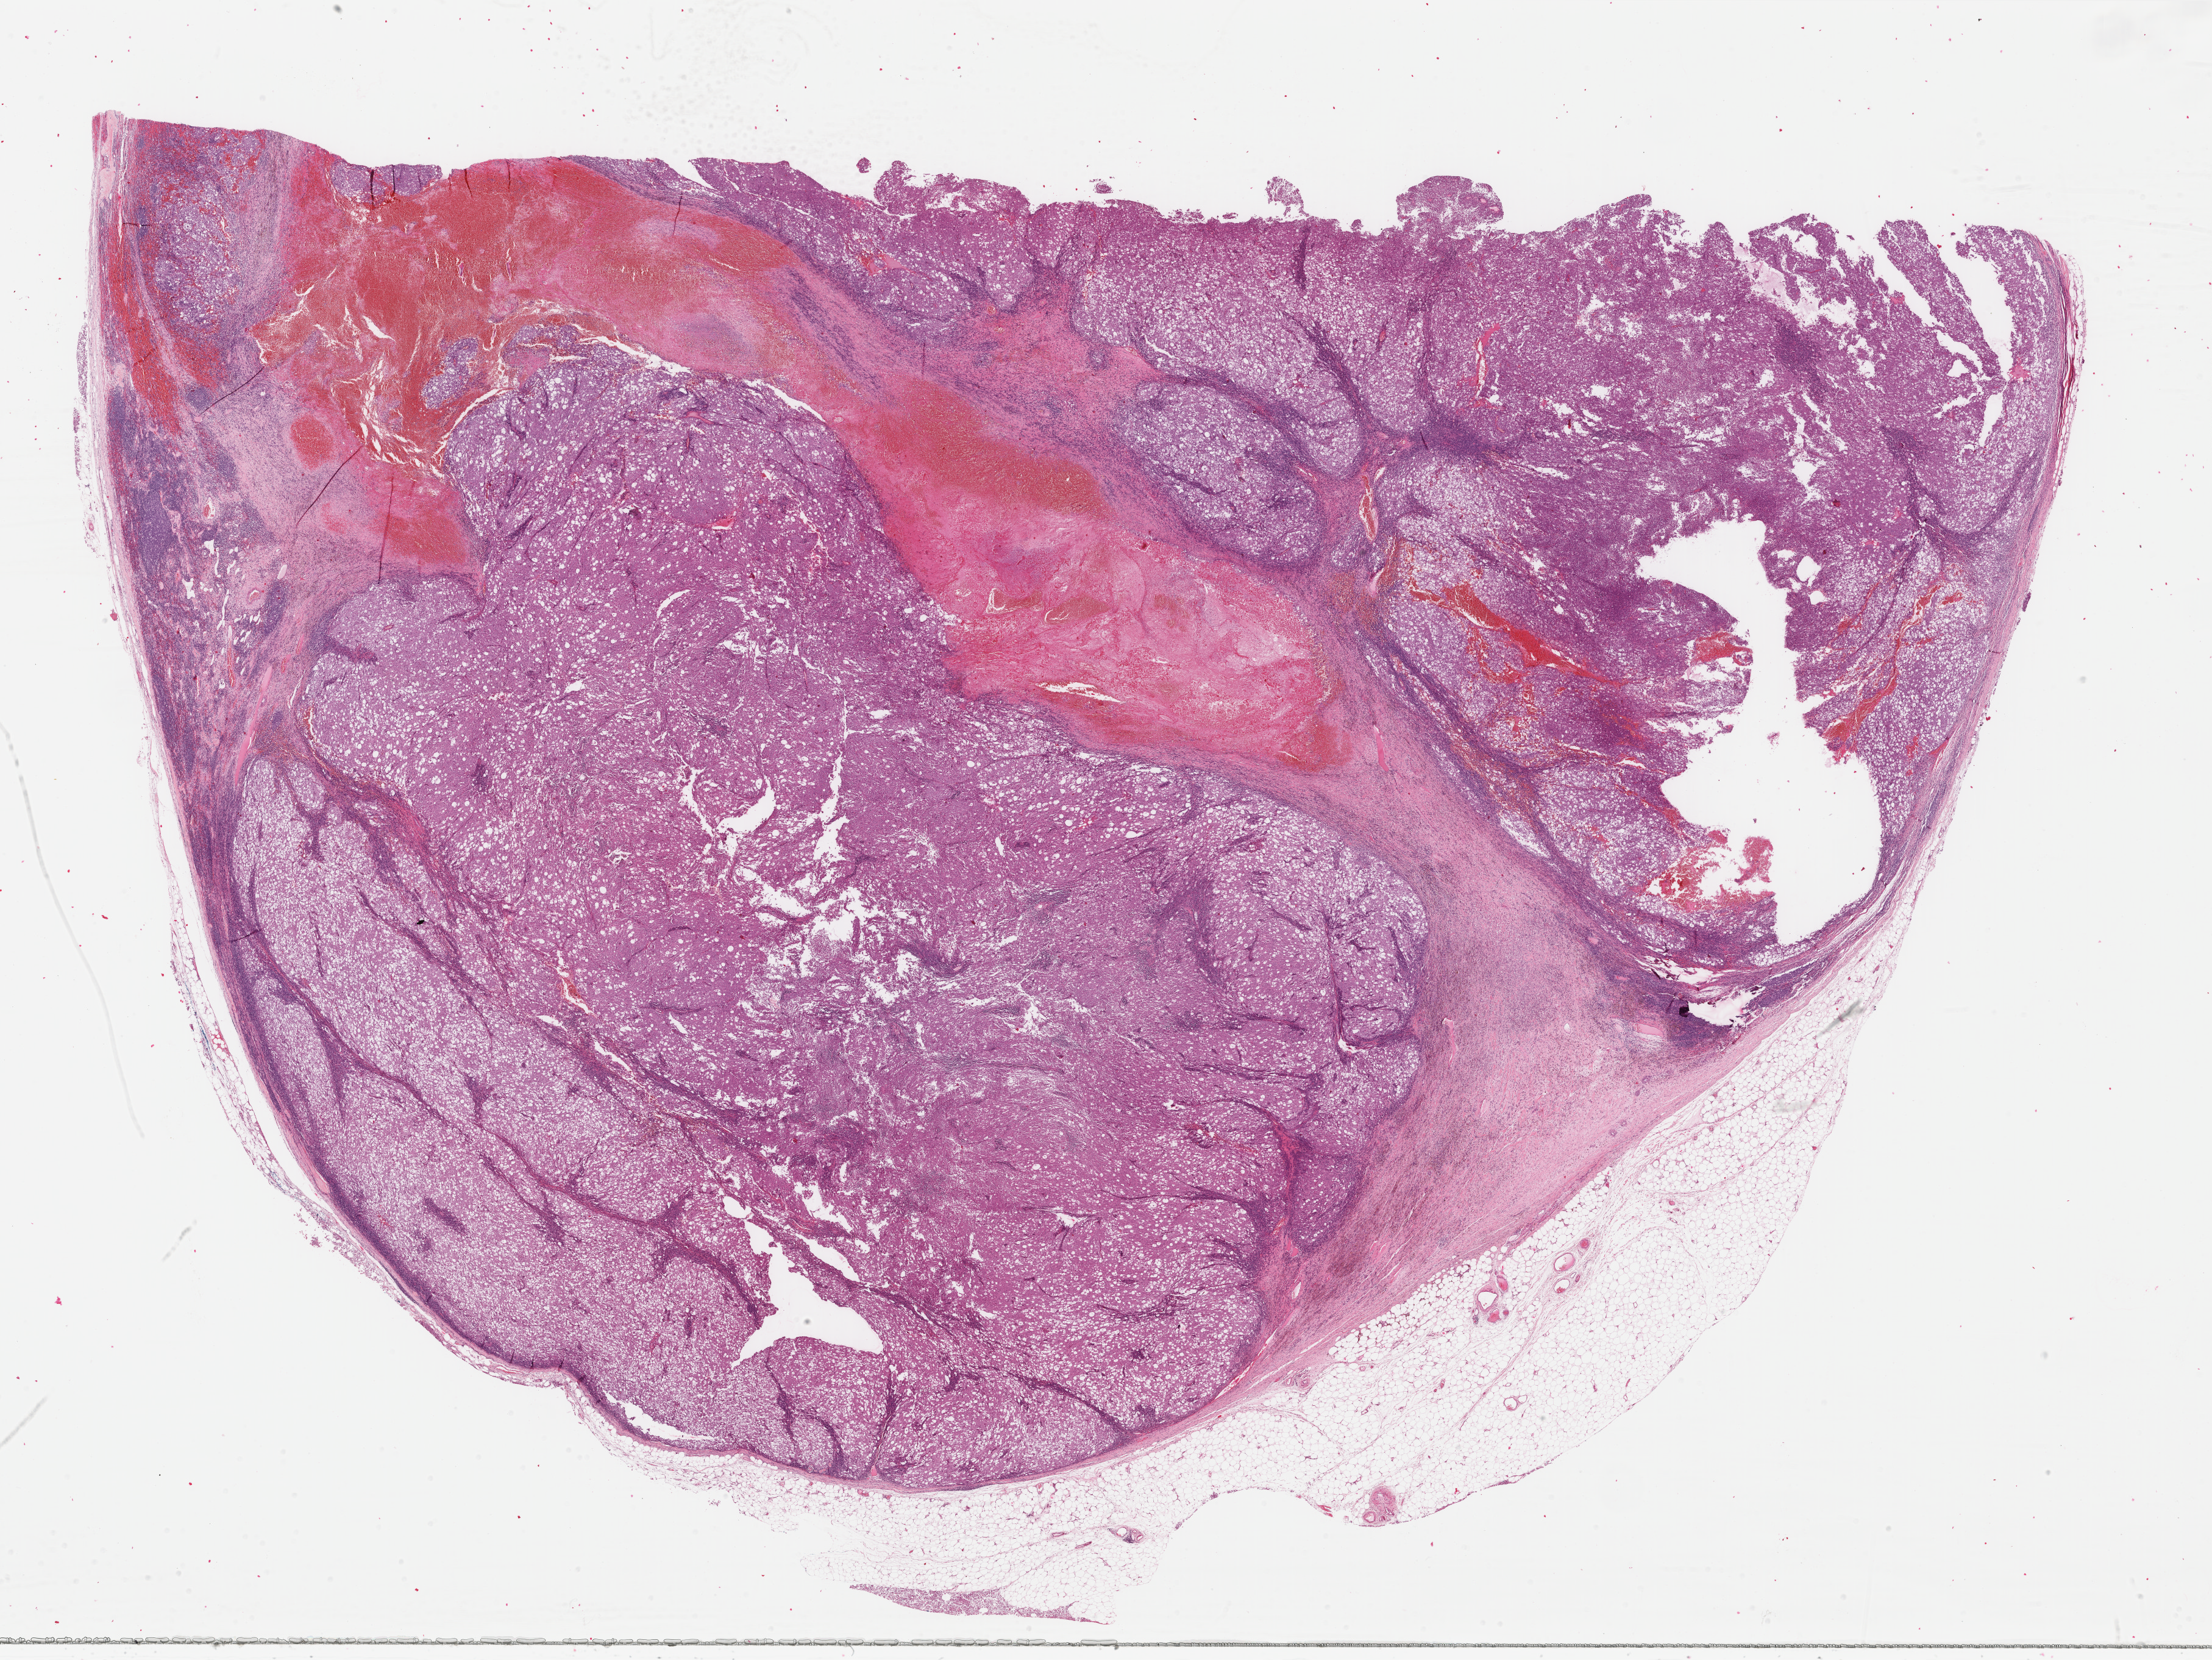
Whole-slide histology image, Hematoxylin and eosin (H&E) stained — a low-resolution overview of the entire scanned area, about 28.8 x 21.6 mm; formalin-fixed paraffin-embedded (FFPE) diagnostic section; primary tumour sample from the skin. Female, age 65 years at initial diagnosis.
Diagnosis: Malignant melanoma, NOS.